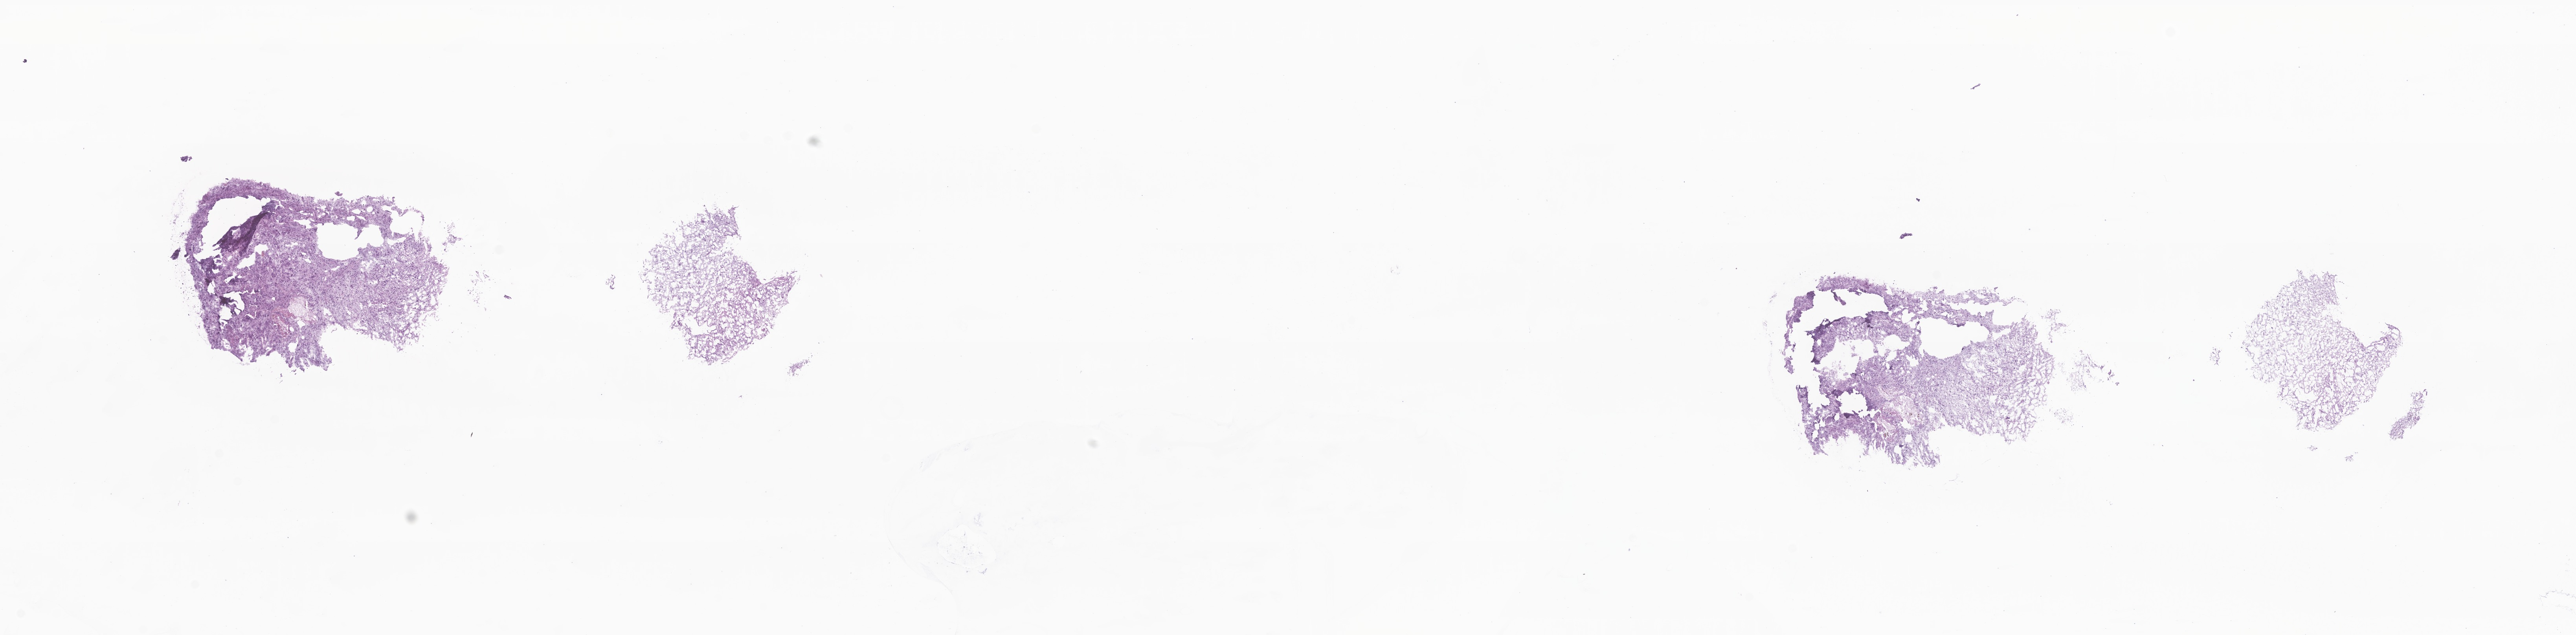
H&E whole-slide image of tumor tissue from the cerebellum, a low-resolution overview of the entire scanned area, about 27.6 x 6.8 mm. Cryosection (OCT / tissue freezing medium). Patient: male, age 197 months.
Diagnosis: Pilocytic astrocytoma.